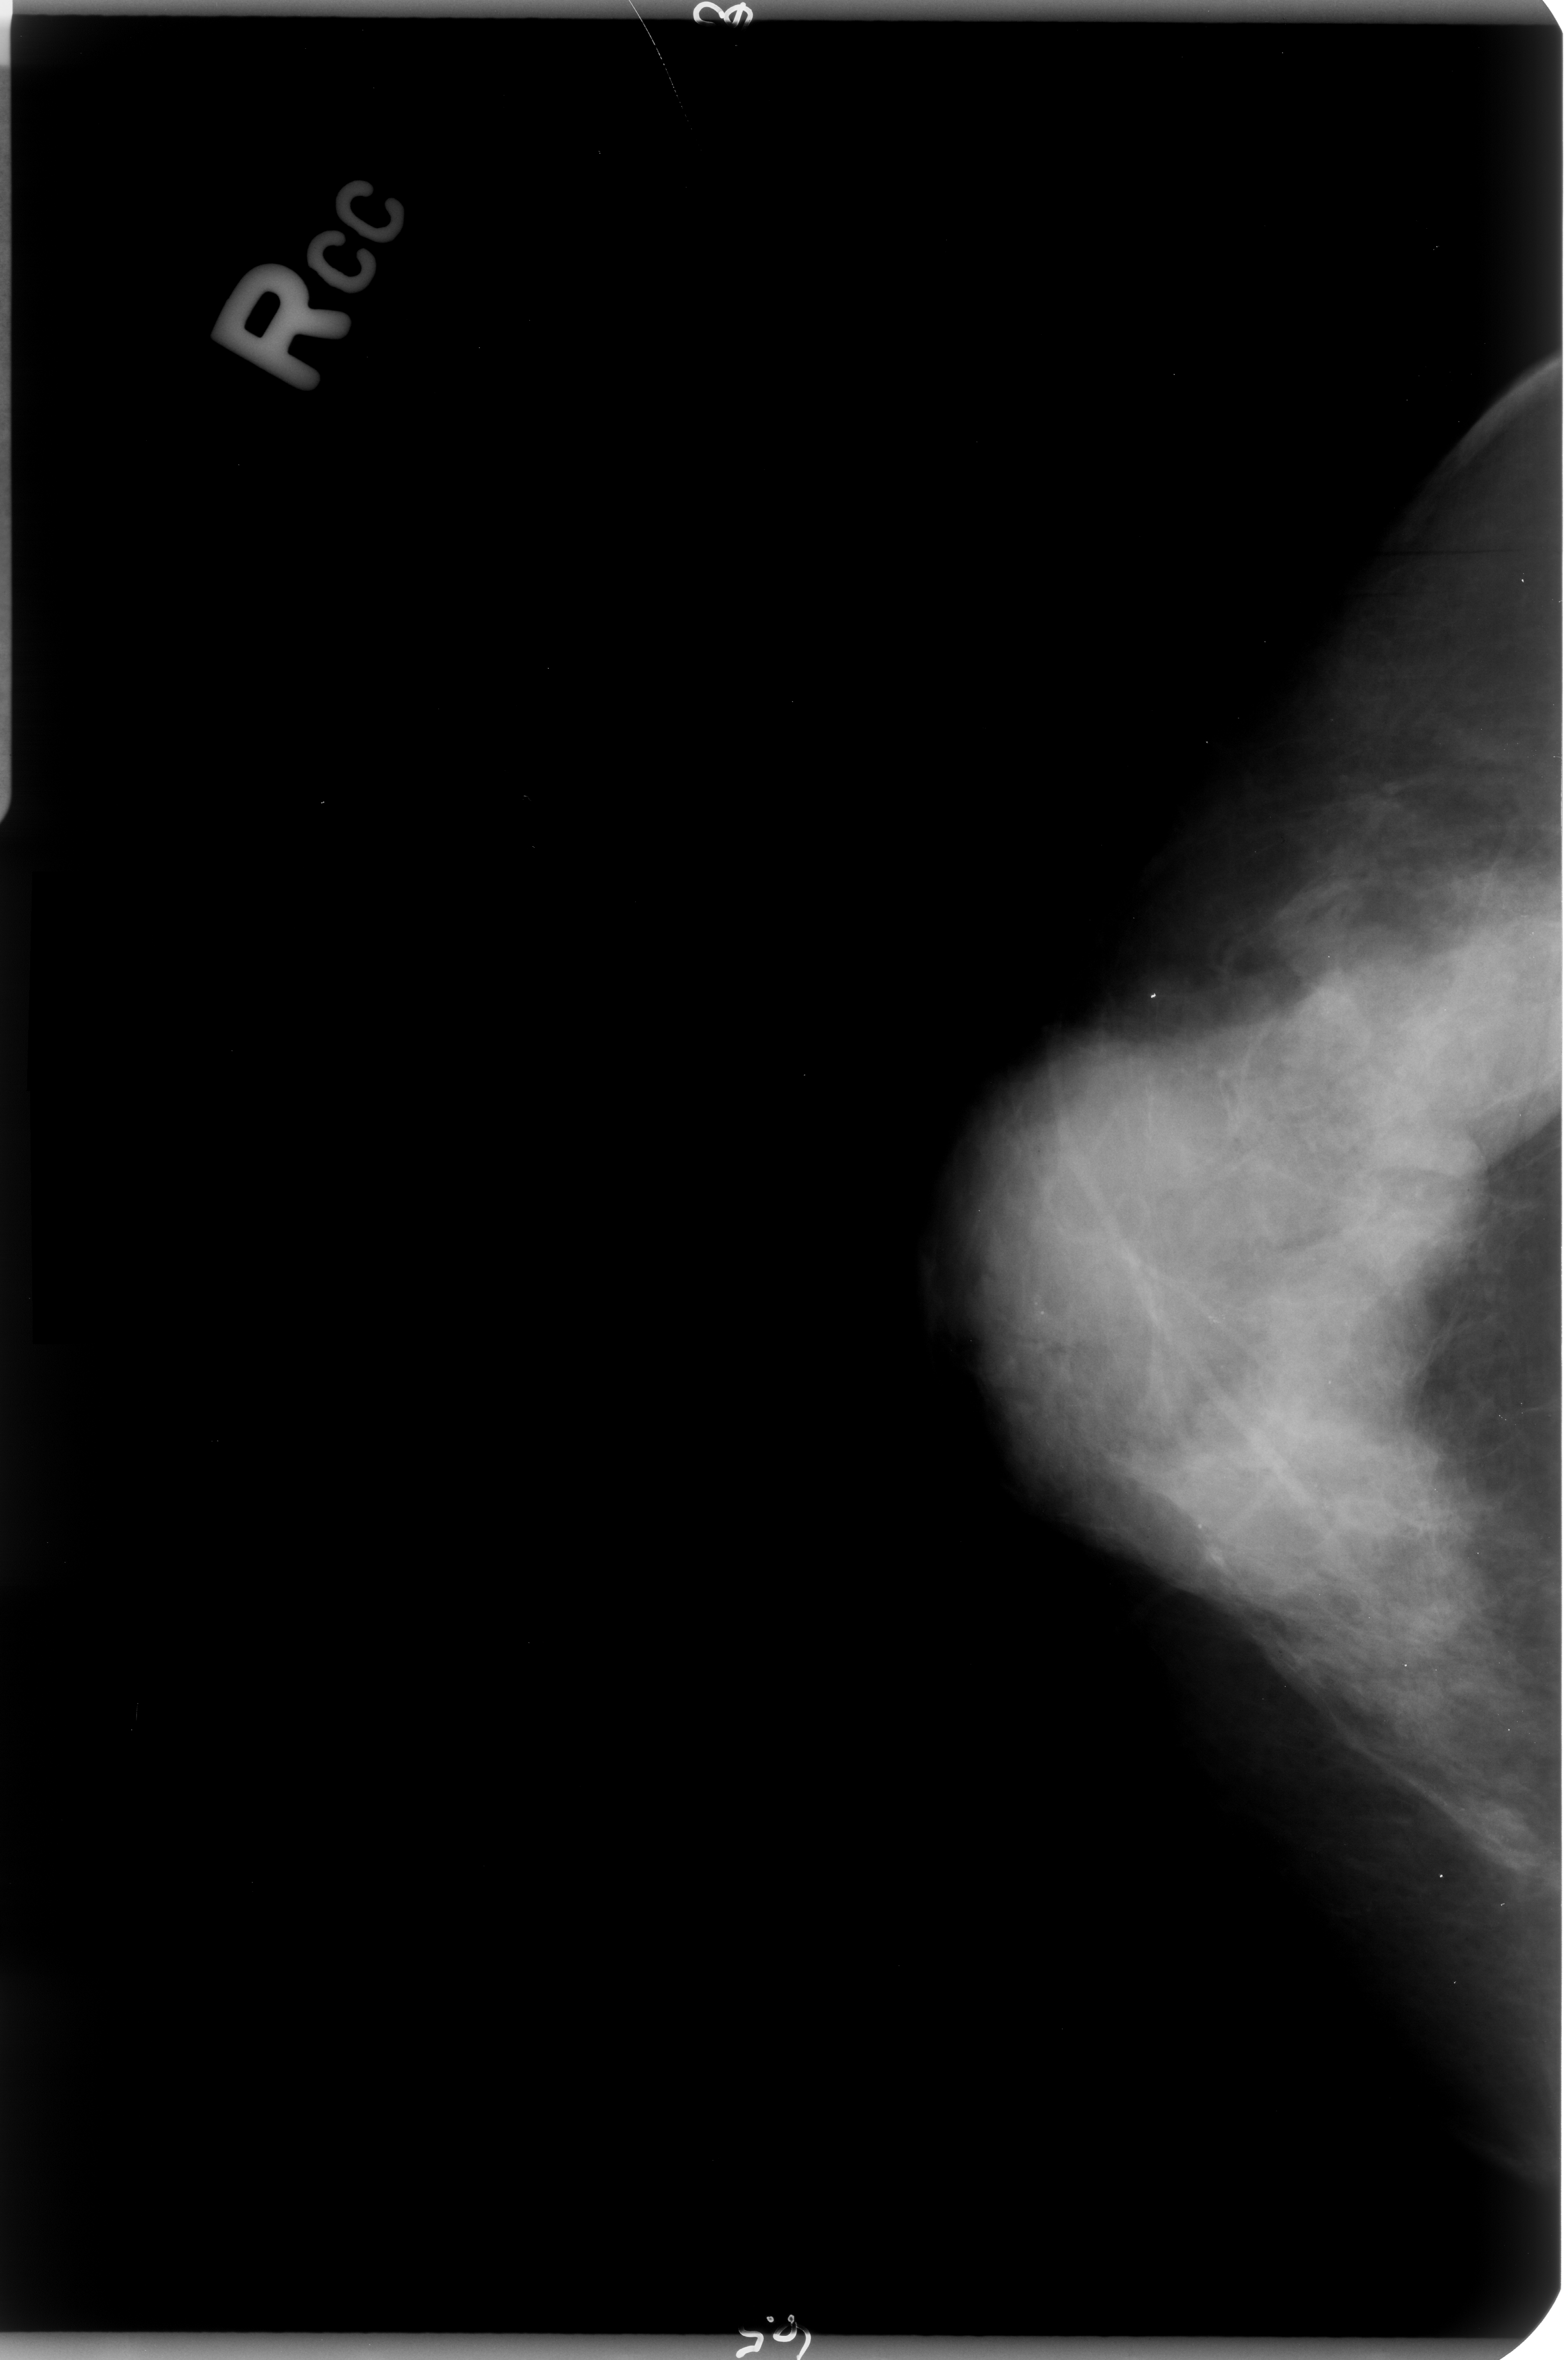
Digitized screen-film mammogram; right breast; CC view; 1568 × 2360 image matrix.
Expert-marked regions of interest on this image (one box per marked abnormality):
- calcifications, morphology pleomorphic, distribution clustered; BI-RADS assessment category 4; pathology result (as recorded, not read from the image): benign: bounding box <1169,1274,1263,1364> (left, top, right, bottom; pixels)